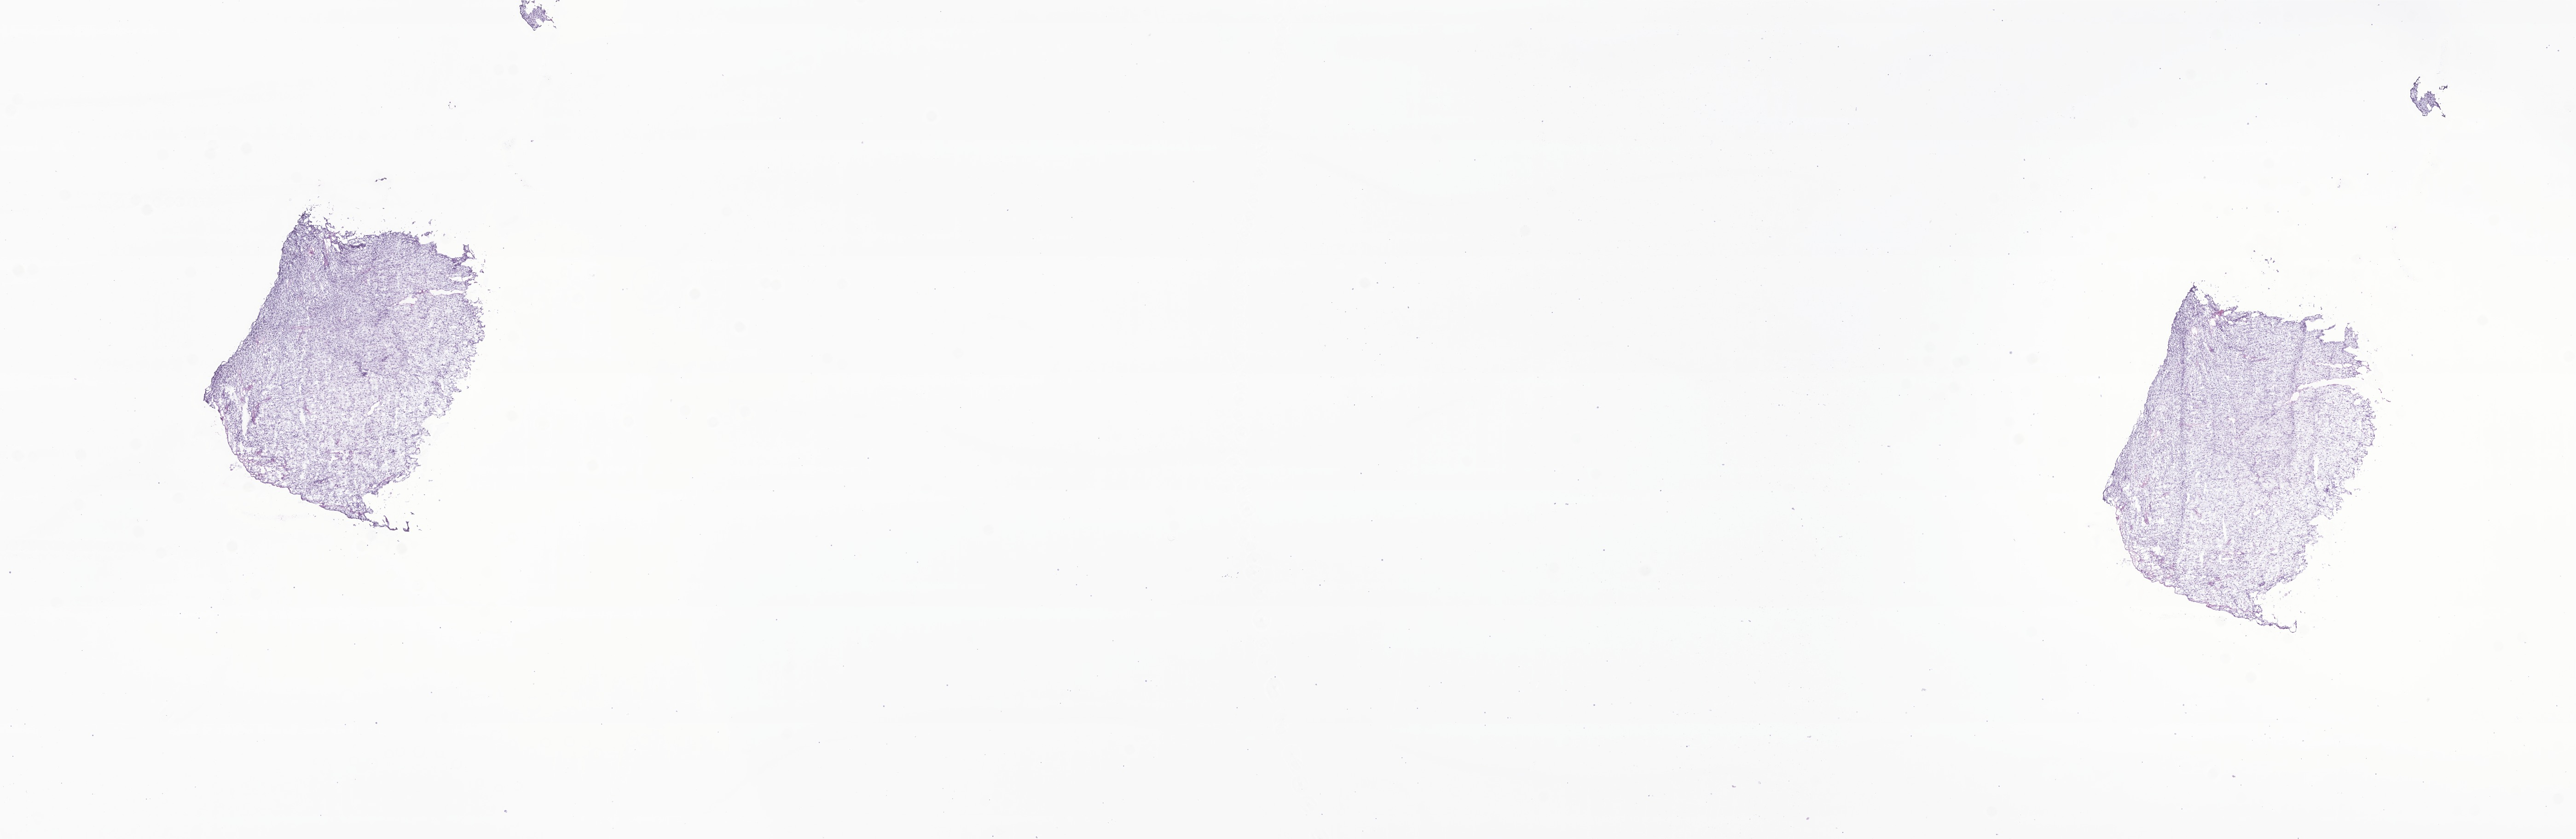
Whole-slide image, haematoxylin and eosin stain of tumor tissue from the urinary bladder, a low-resolution overview of the entire scanned area, about 23.6 x 7.7 mm, frozen section. Male patient, age 55 months (4 years 7 months).
* recorded diagnosis: Embryonal rhabdomyosarcoma, NOS